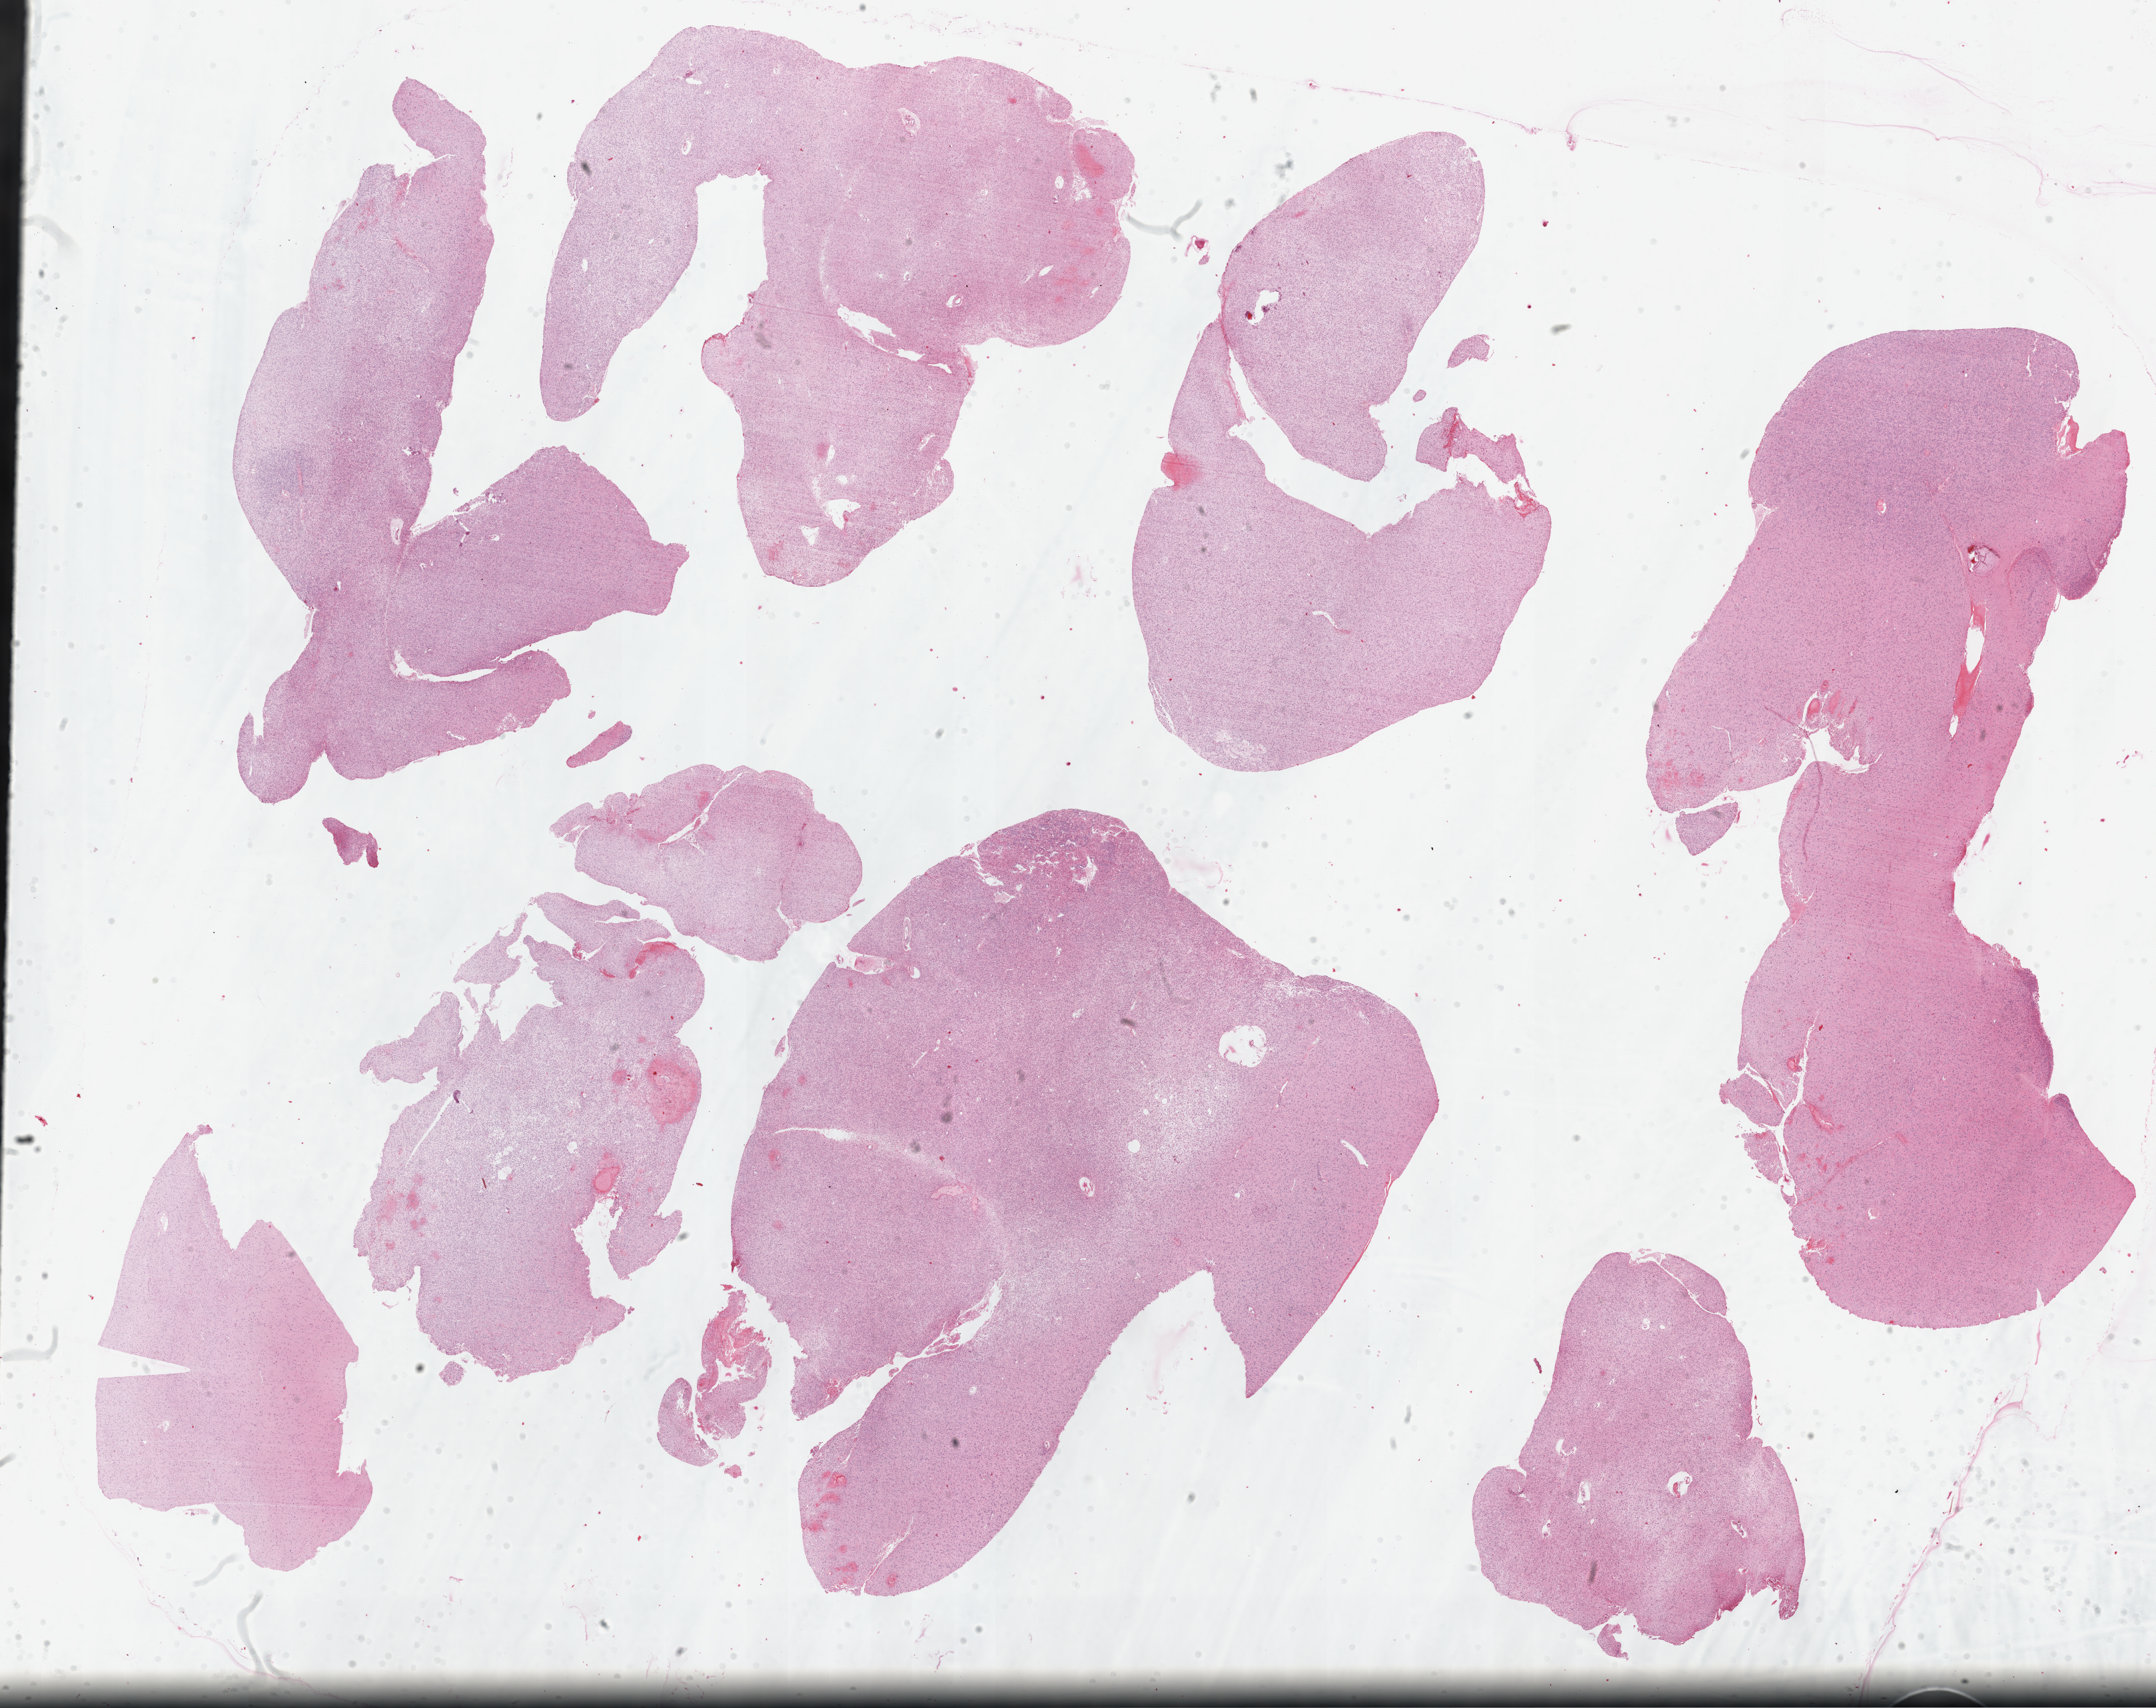
Whole-slide histology image, H&E — shown as a low-resolution overview of the whole scanned area (about 26.2 x 20.7 mm, from a 40x scan); formalin-fixed paraffin-embedded (FFPE) diagnostic section; sample: primary tumour, brain. Patient: male, age at initial diagnosis 47 years.
Pathologic diagnosis: Mixed glioma (cerebrum).